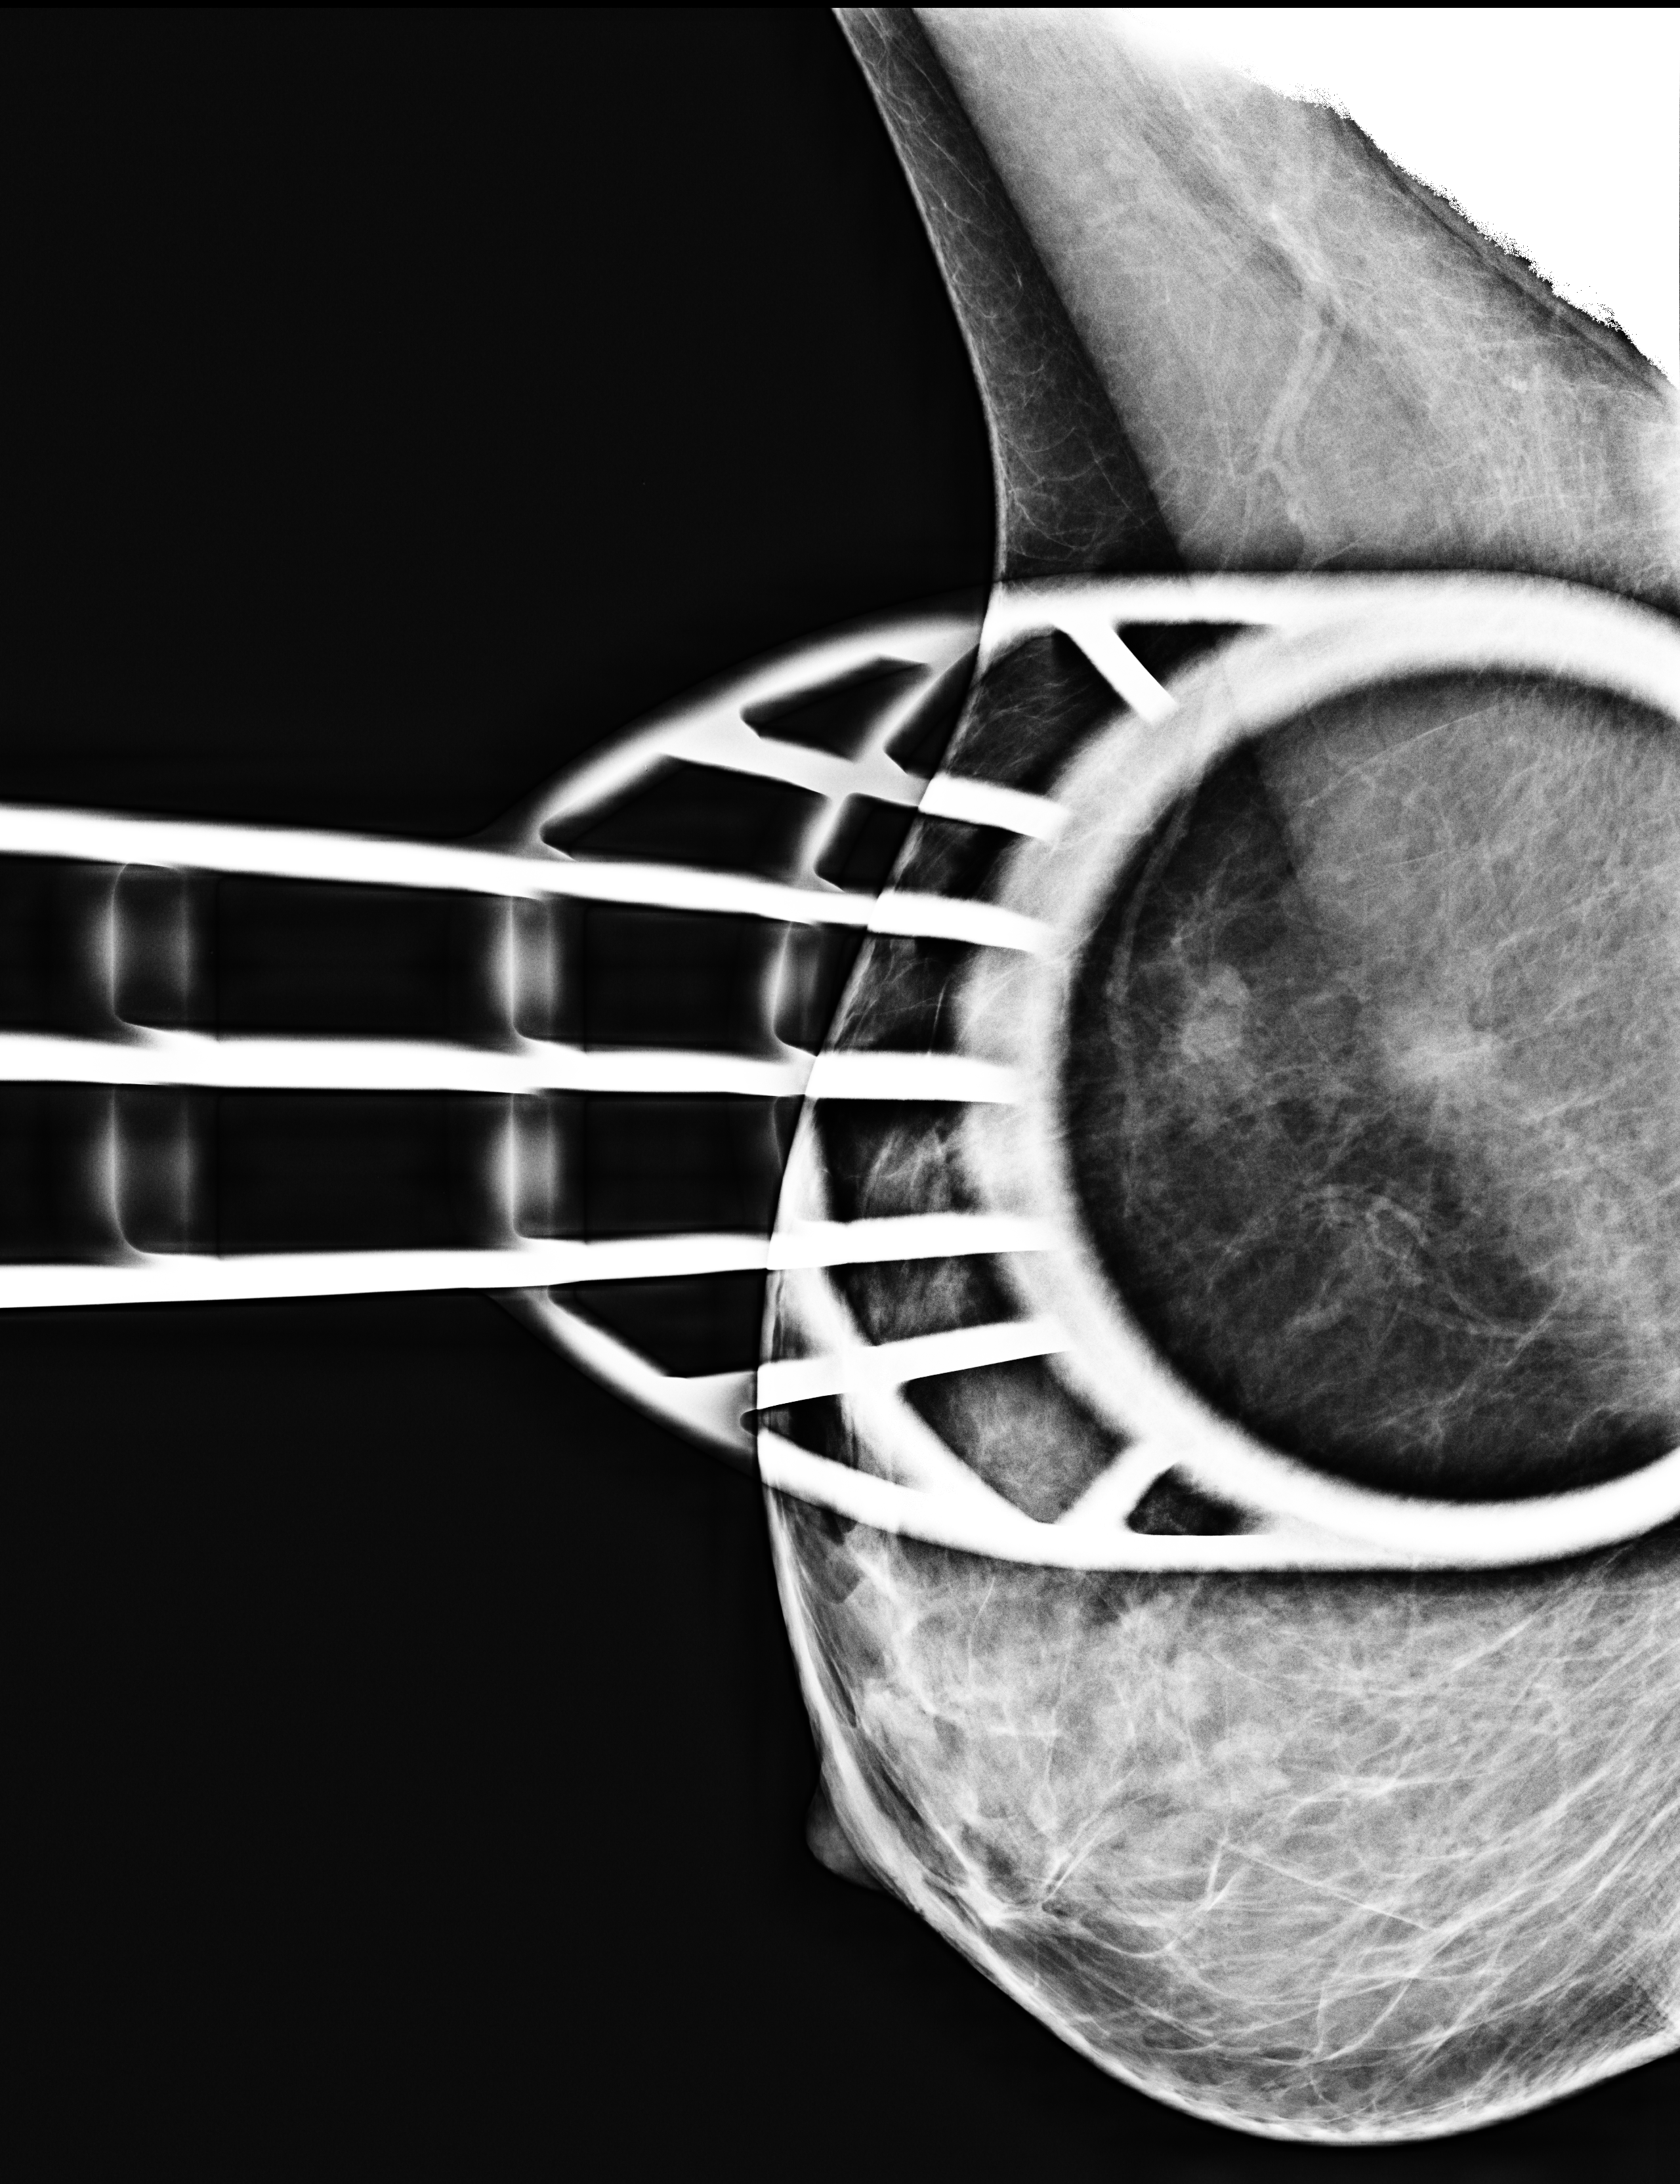
Additional work-up view.
Image type: full-field digital mammogram. Breast: right. Projection: mediolateral oblique (MLO) view, spot compression.